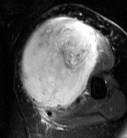
MRI of an extremity soft-tissue mass, one axial slice. Position 43 of 87 along the scan axis. T2-weighted fat-saturated. MR volume resampled by the dataset authors to the PET/CT grid (not the native acquisition matrix). 127 × 138 image matrix. Female patient. Case-level facts recorded for this patient, not image findings: histological type: pleiomorphic leiomyosarcoma; grade: high; site of the primary tumour: left biceps.
Annotated regions visible in this slice (expert contour drawn on MRI and transferred to this co-registered scan by the dataset authors):
- gross tumour volume including surrounding oedema: bounding box (x1, y1, x2, y2) in pixels: (20, 16, 105, 113)
- gross tumour volume (mass): (20, 16, 99, 111)